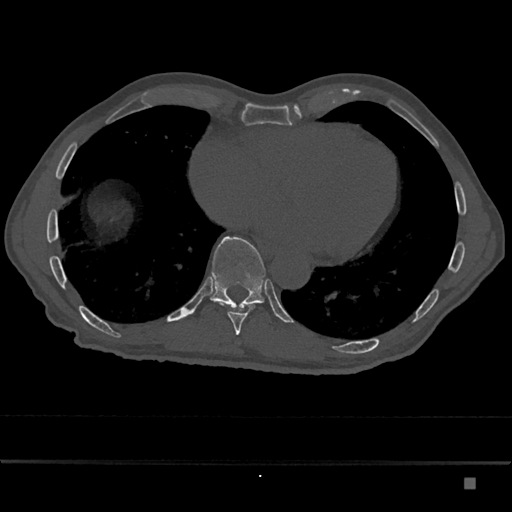
CT including the spine, one axial slice; position 773 of 797 along the scan axis; reconstruction kernel Br40s/3; 120 kVp; bone window (W 1800 / L 400 HU); 0.5 mm slice thickness; 512 × 512 image matrix. Male patient, age 72 years. From the clinical record (not read from this slice): primary cancer: prostate.
Outlined on this slice (semi-automatically segmented with operator editing):
- T10 vertebra: bounding box <210,237,266,310> (left, top, right, bottom; pixels)
- T9 vertebra: <228,304,253,335>